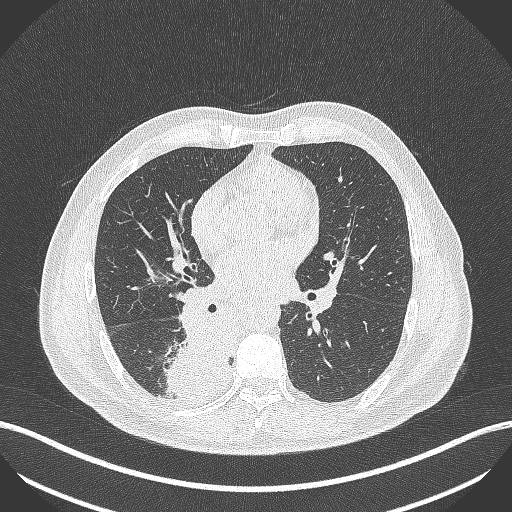
Chest CT, one axial slice. Slice 236 of 451 in the series (ordered by position). Reconstruction kernel B70f. 100 kVp. Lung window (W 1500 / L -600 HU). 1 mm slice thickness. 512 × 512 image matrix, field of view 400 × 400 mm. Patient: male, 61 years. Case-level facts recorded for this patient, not image findings: clinical TNM (as recorded): T1 N0 M0; histopathological grade: G3.
Structures marked on this image (rectangle marked by the reading radiologist):
- lung tumour (recorded histology: small cell carcinoma): bounding box (x1, y1, x2, y2) in pixels: (163, 315, 230, 403)